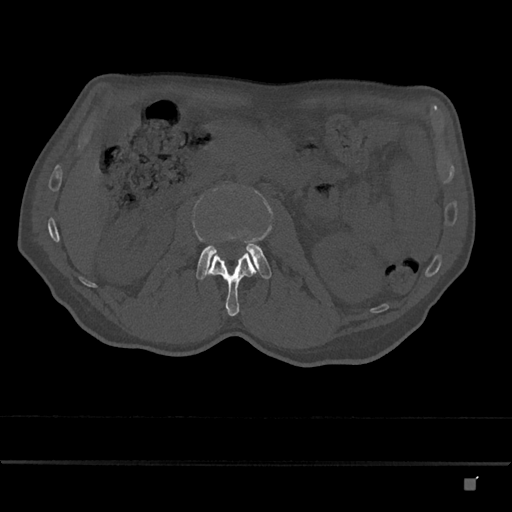
CT including the spine, one axial slice. Position 445 of 797 along the scan axis. Reconstruction kernel Br40s/3. Bone window (W 1800 / L 400 HU). 0.5 mm slice thickness. 512 × 512 image matrix, field of view 390 × 390 mm. Patient: male, 72 years. From the clinical record (not read from this slice): primary cancer: prostate.
Annotated regions visible in this slice (semi-automatic segmentation, software-assisted and operator-edited):
- L2 vertebra: bounding box <206,252,256,317> (left, top, right, bottom; pixels)
- L3 vertebra: <196,243,272,280>